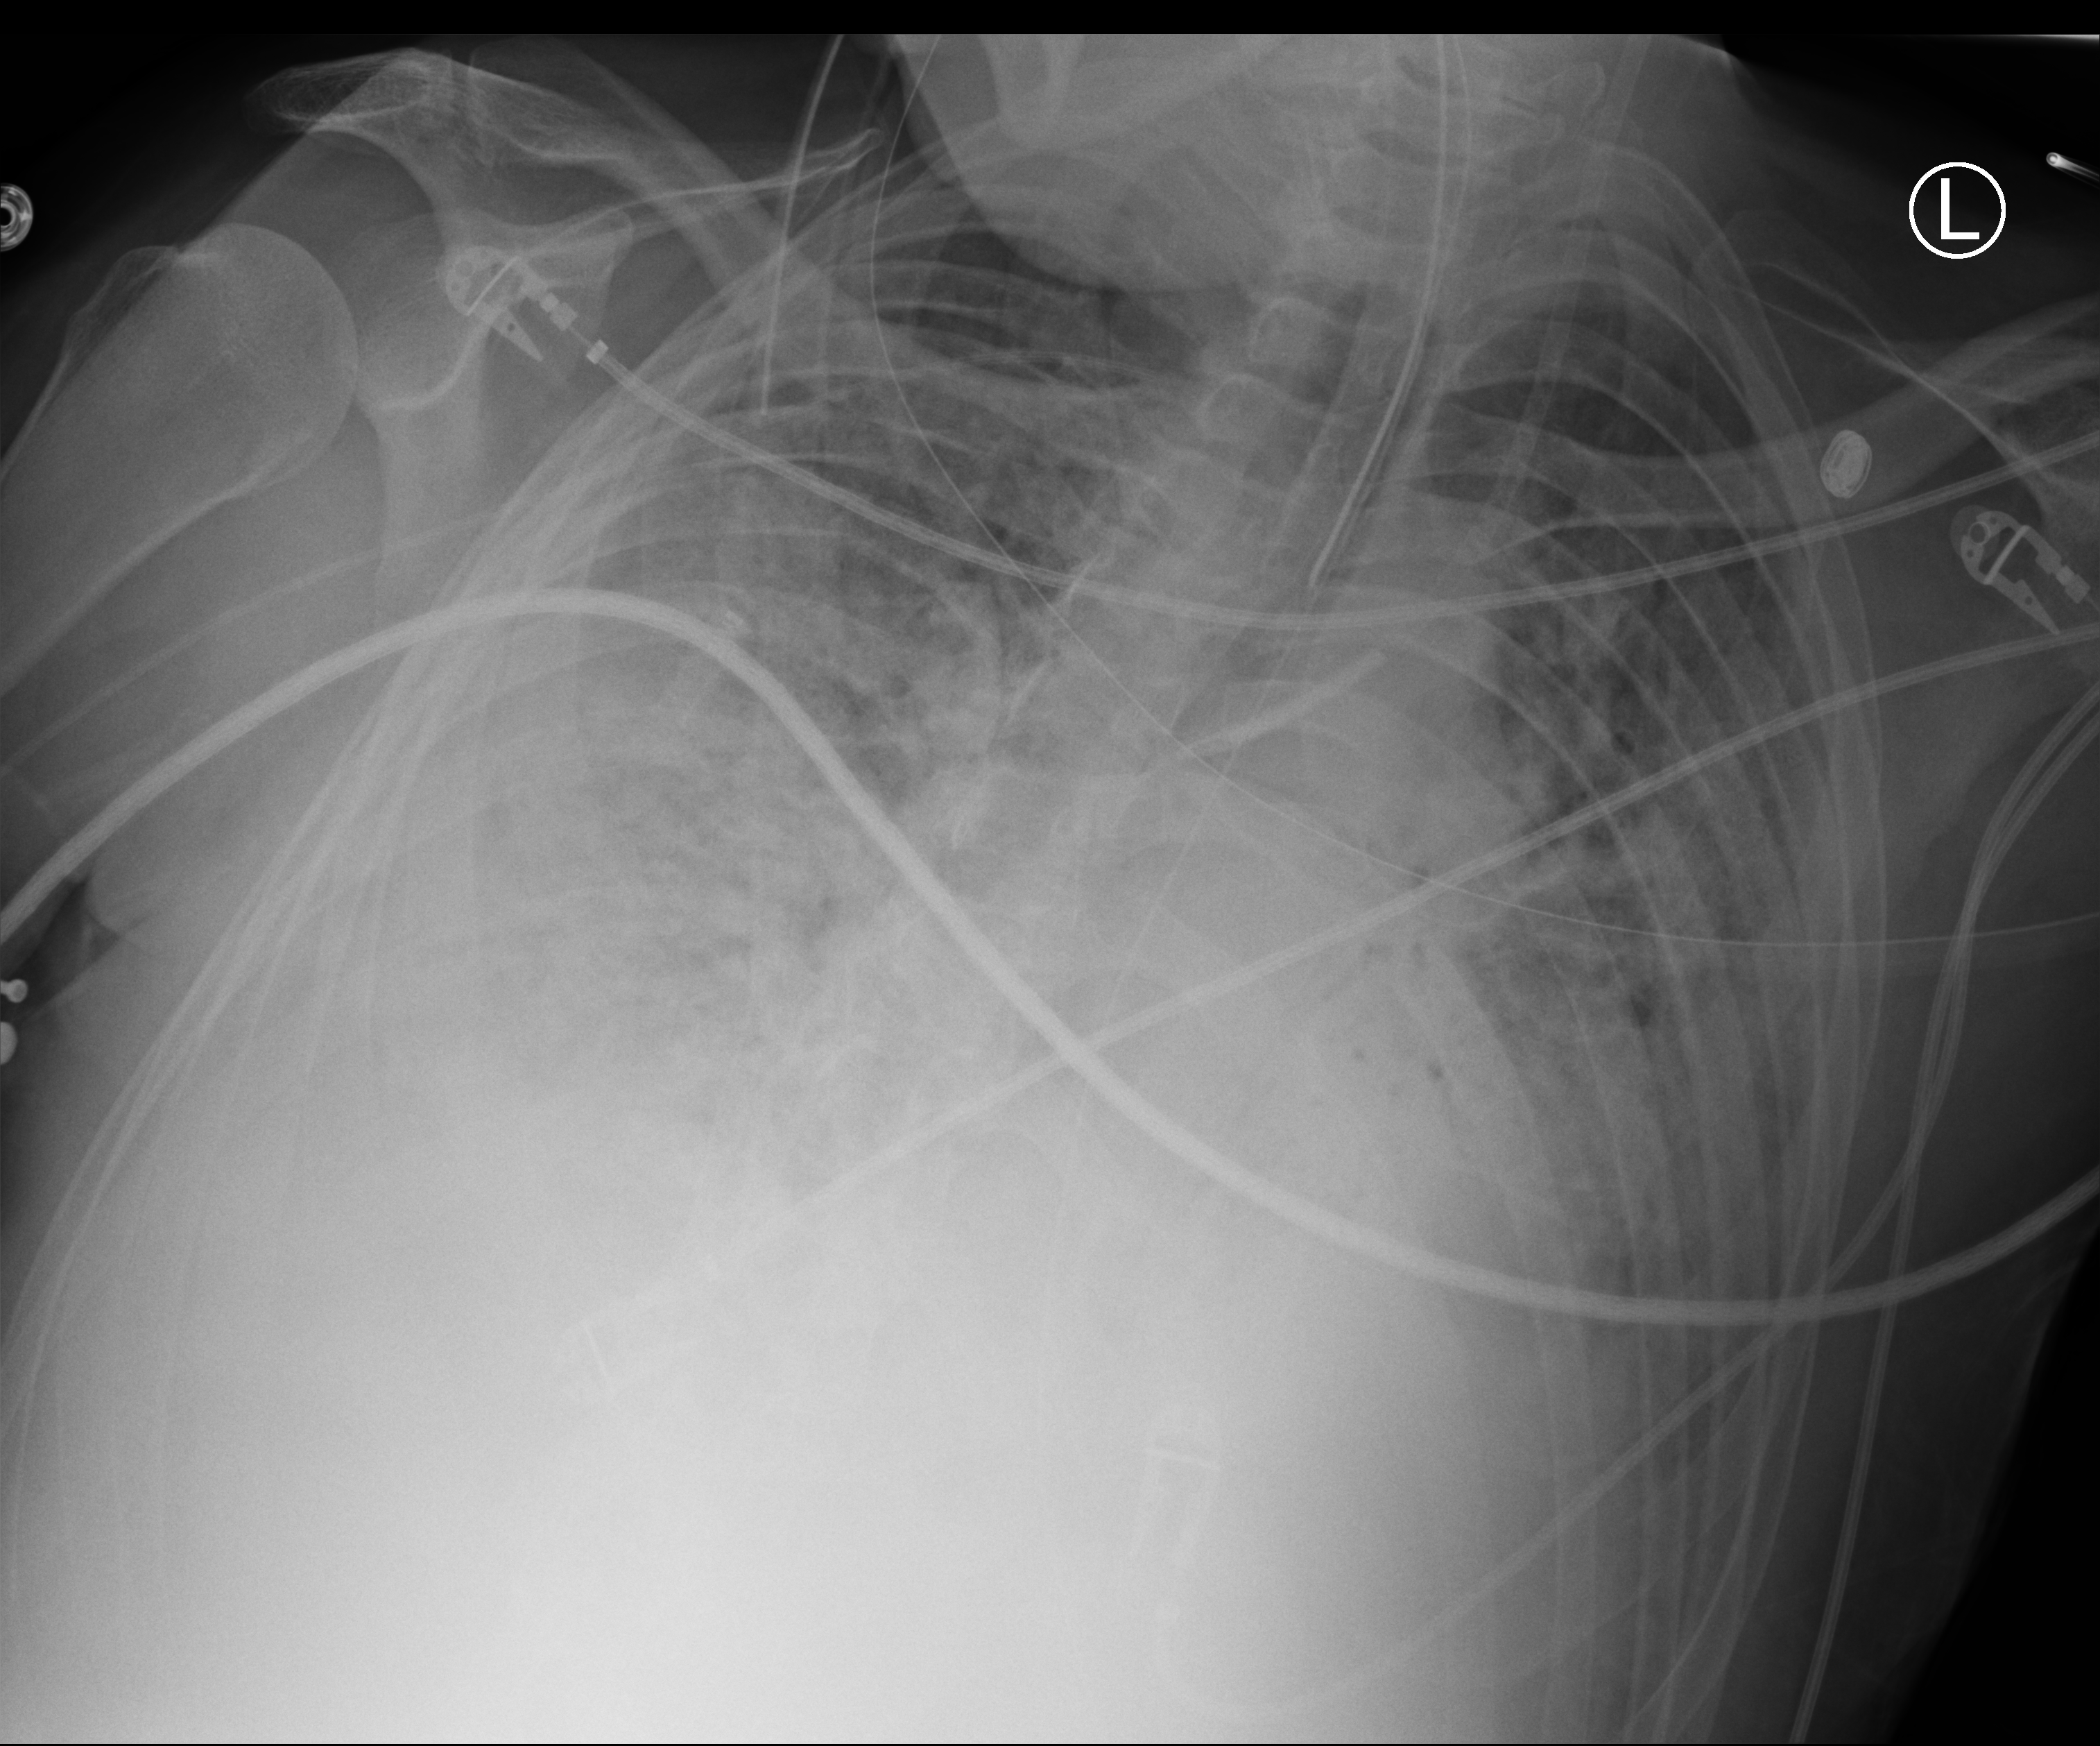
Chest X-ray (portable), anteroposterior (AP) projection. Patient hospitalised with COVID-19; male, aged 18–59 years.
Admission-level facts for this patient (not findings on this image; timing relative to this image not recorded): diabetes (admission record): no.